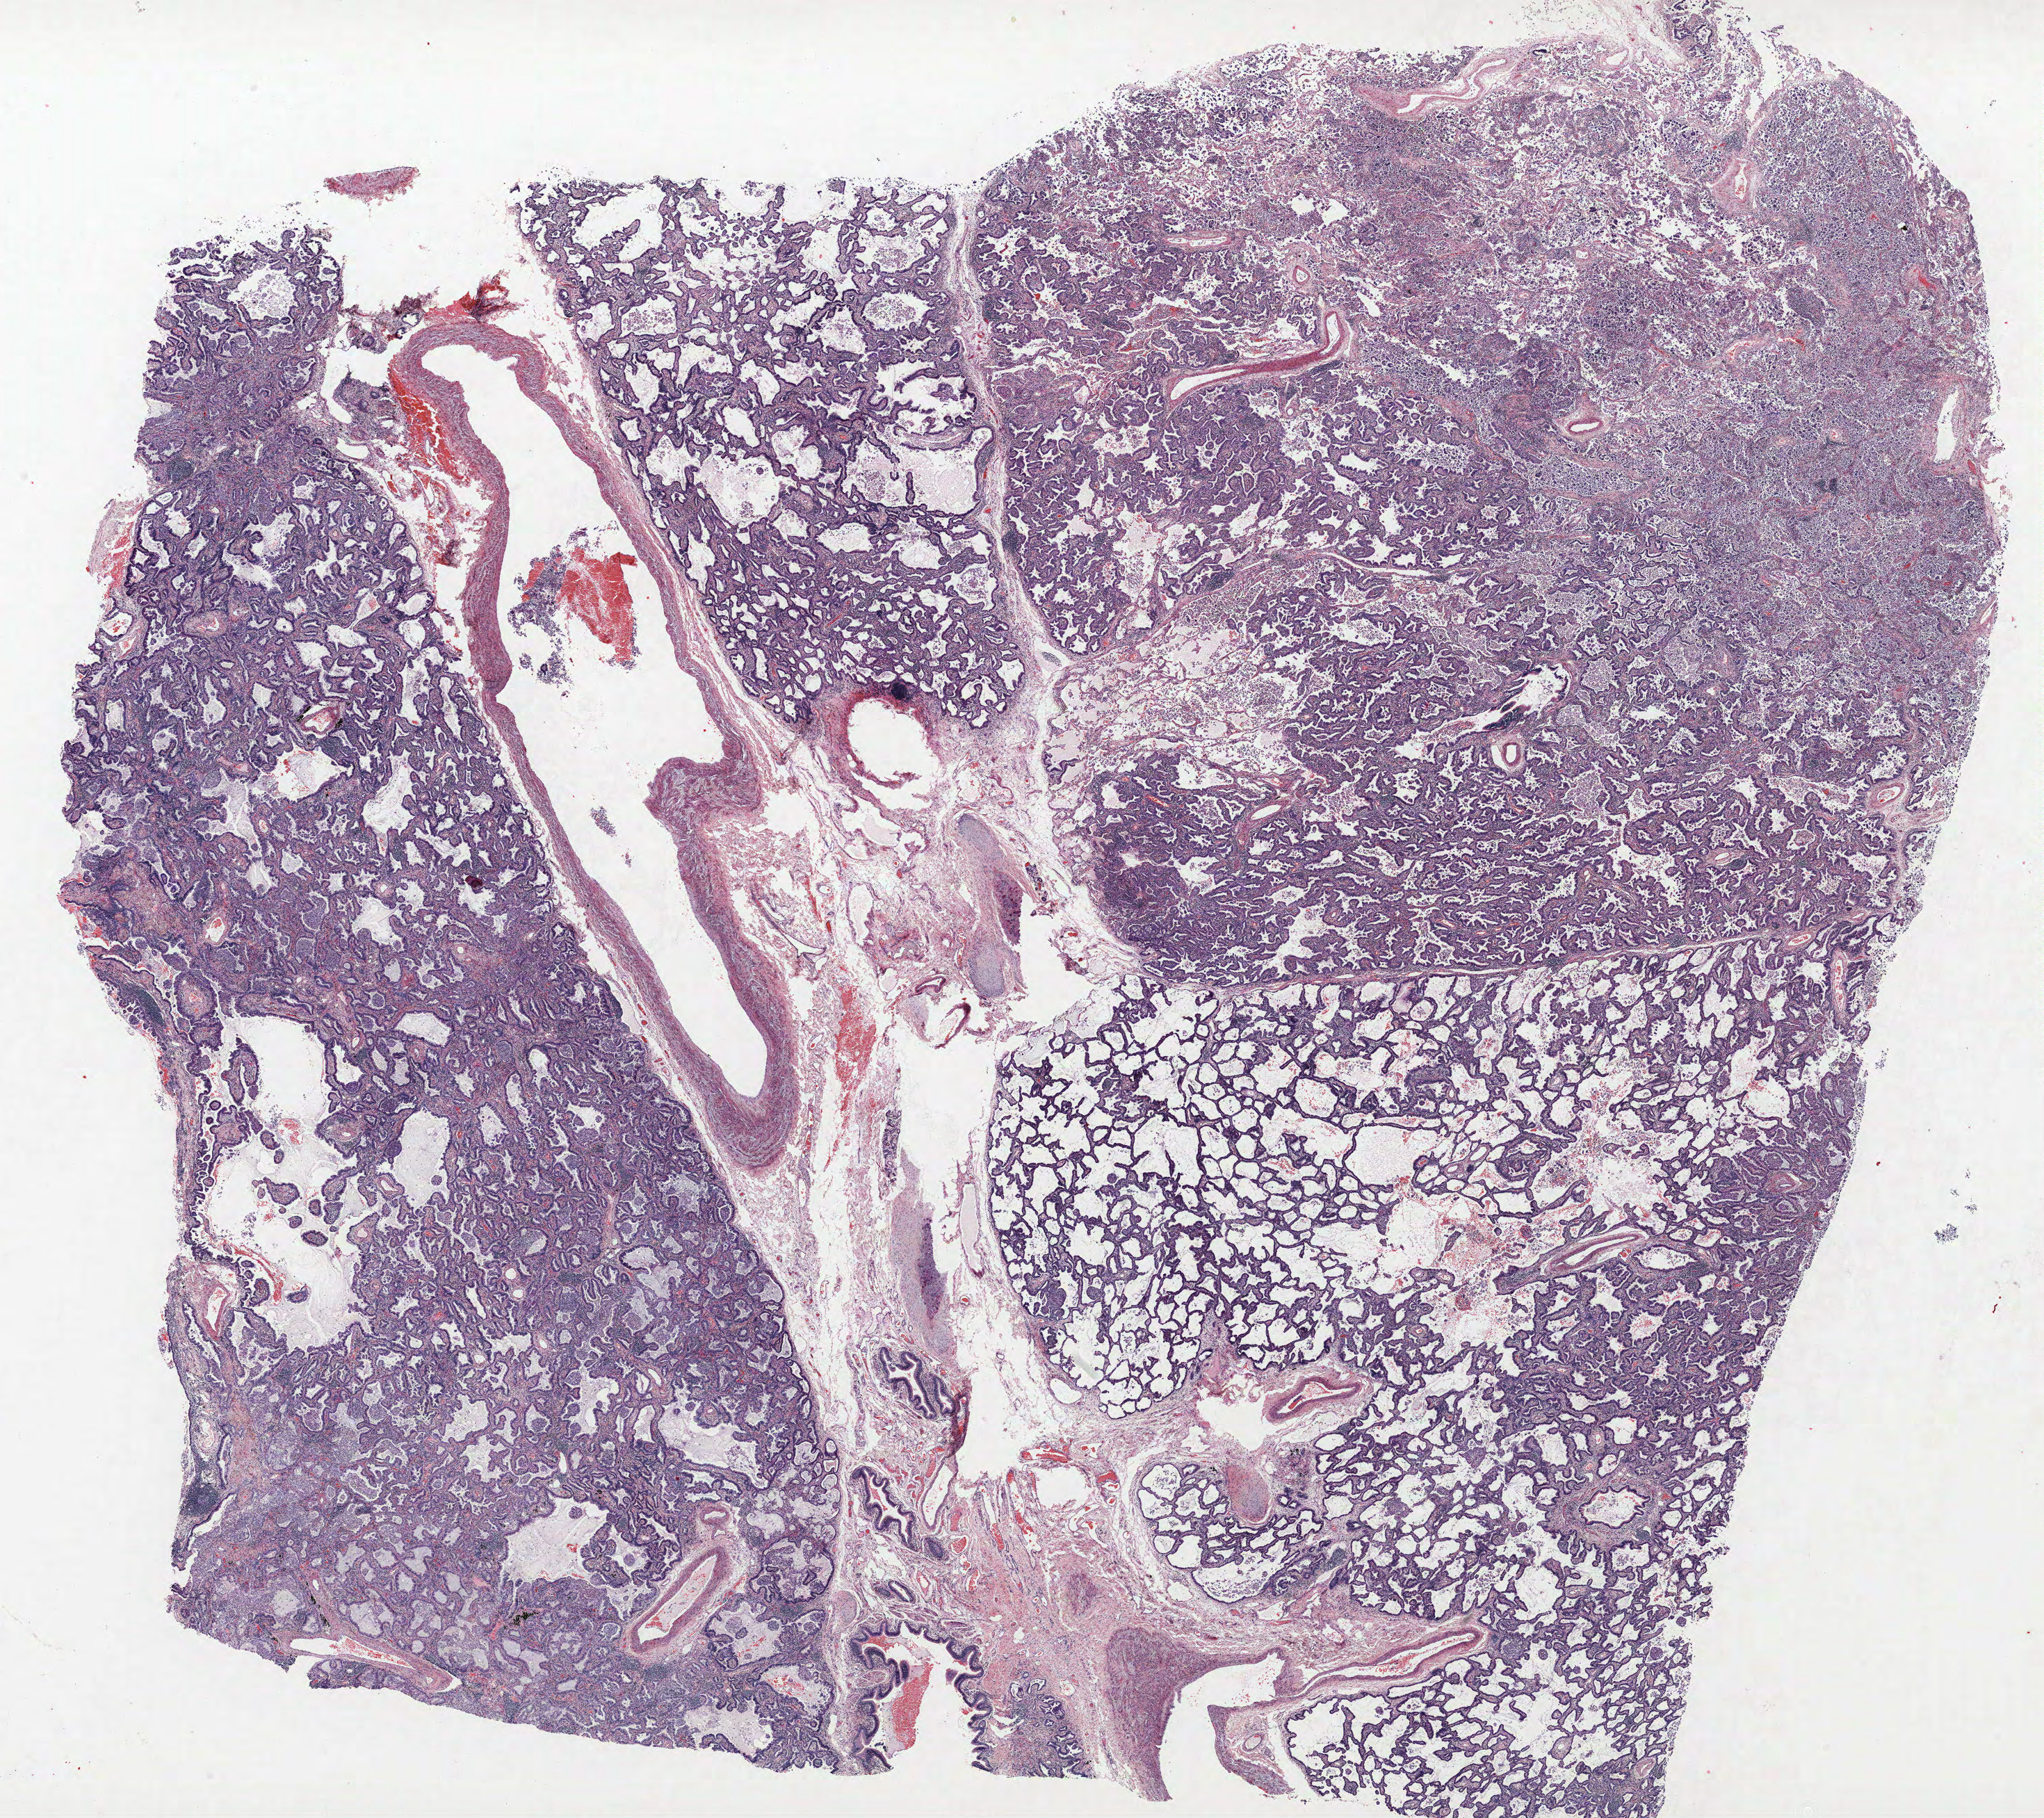
H&E-stained whole-slide image, a low-resolution overview of the entire scanned area, about 23.5 x 20.9 mm (from a 40x scan), FFPE section, lung tissue. Female, age 73 at enrolment. Grade: well differentiated (G1).
Participant's lung-cancer diagnosis: Mucinous adenocarcinoma (ICD-O-3 8480/3). Stage (AJCC 6th edition): IV. Tumour size (pathology): 85 mm. Primary tumour location (clinical record): right lower lobe.